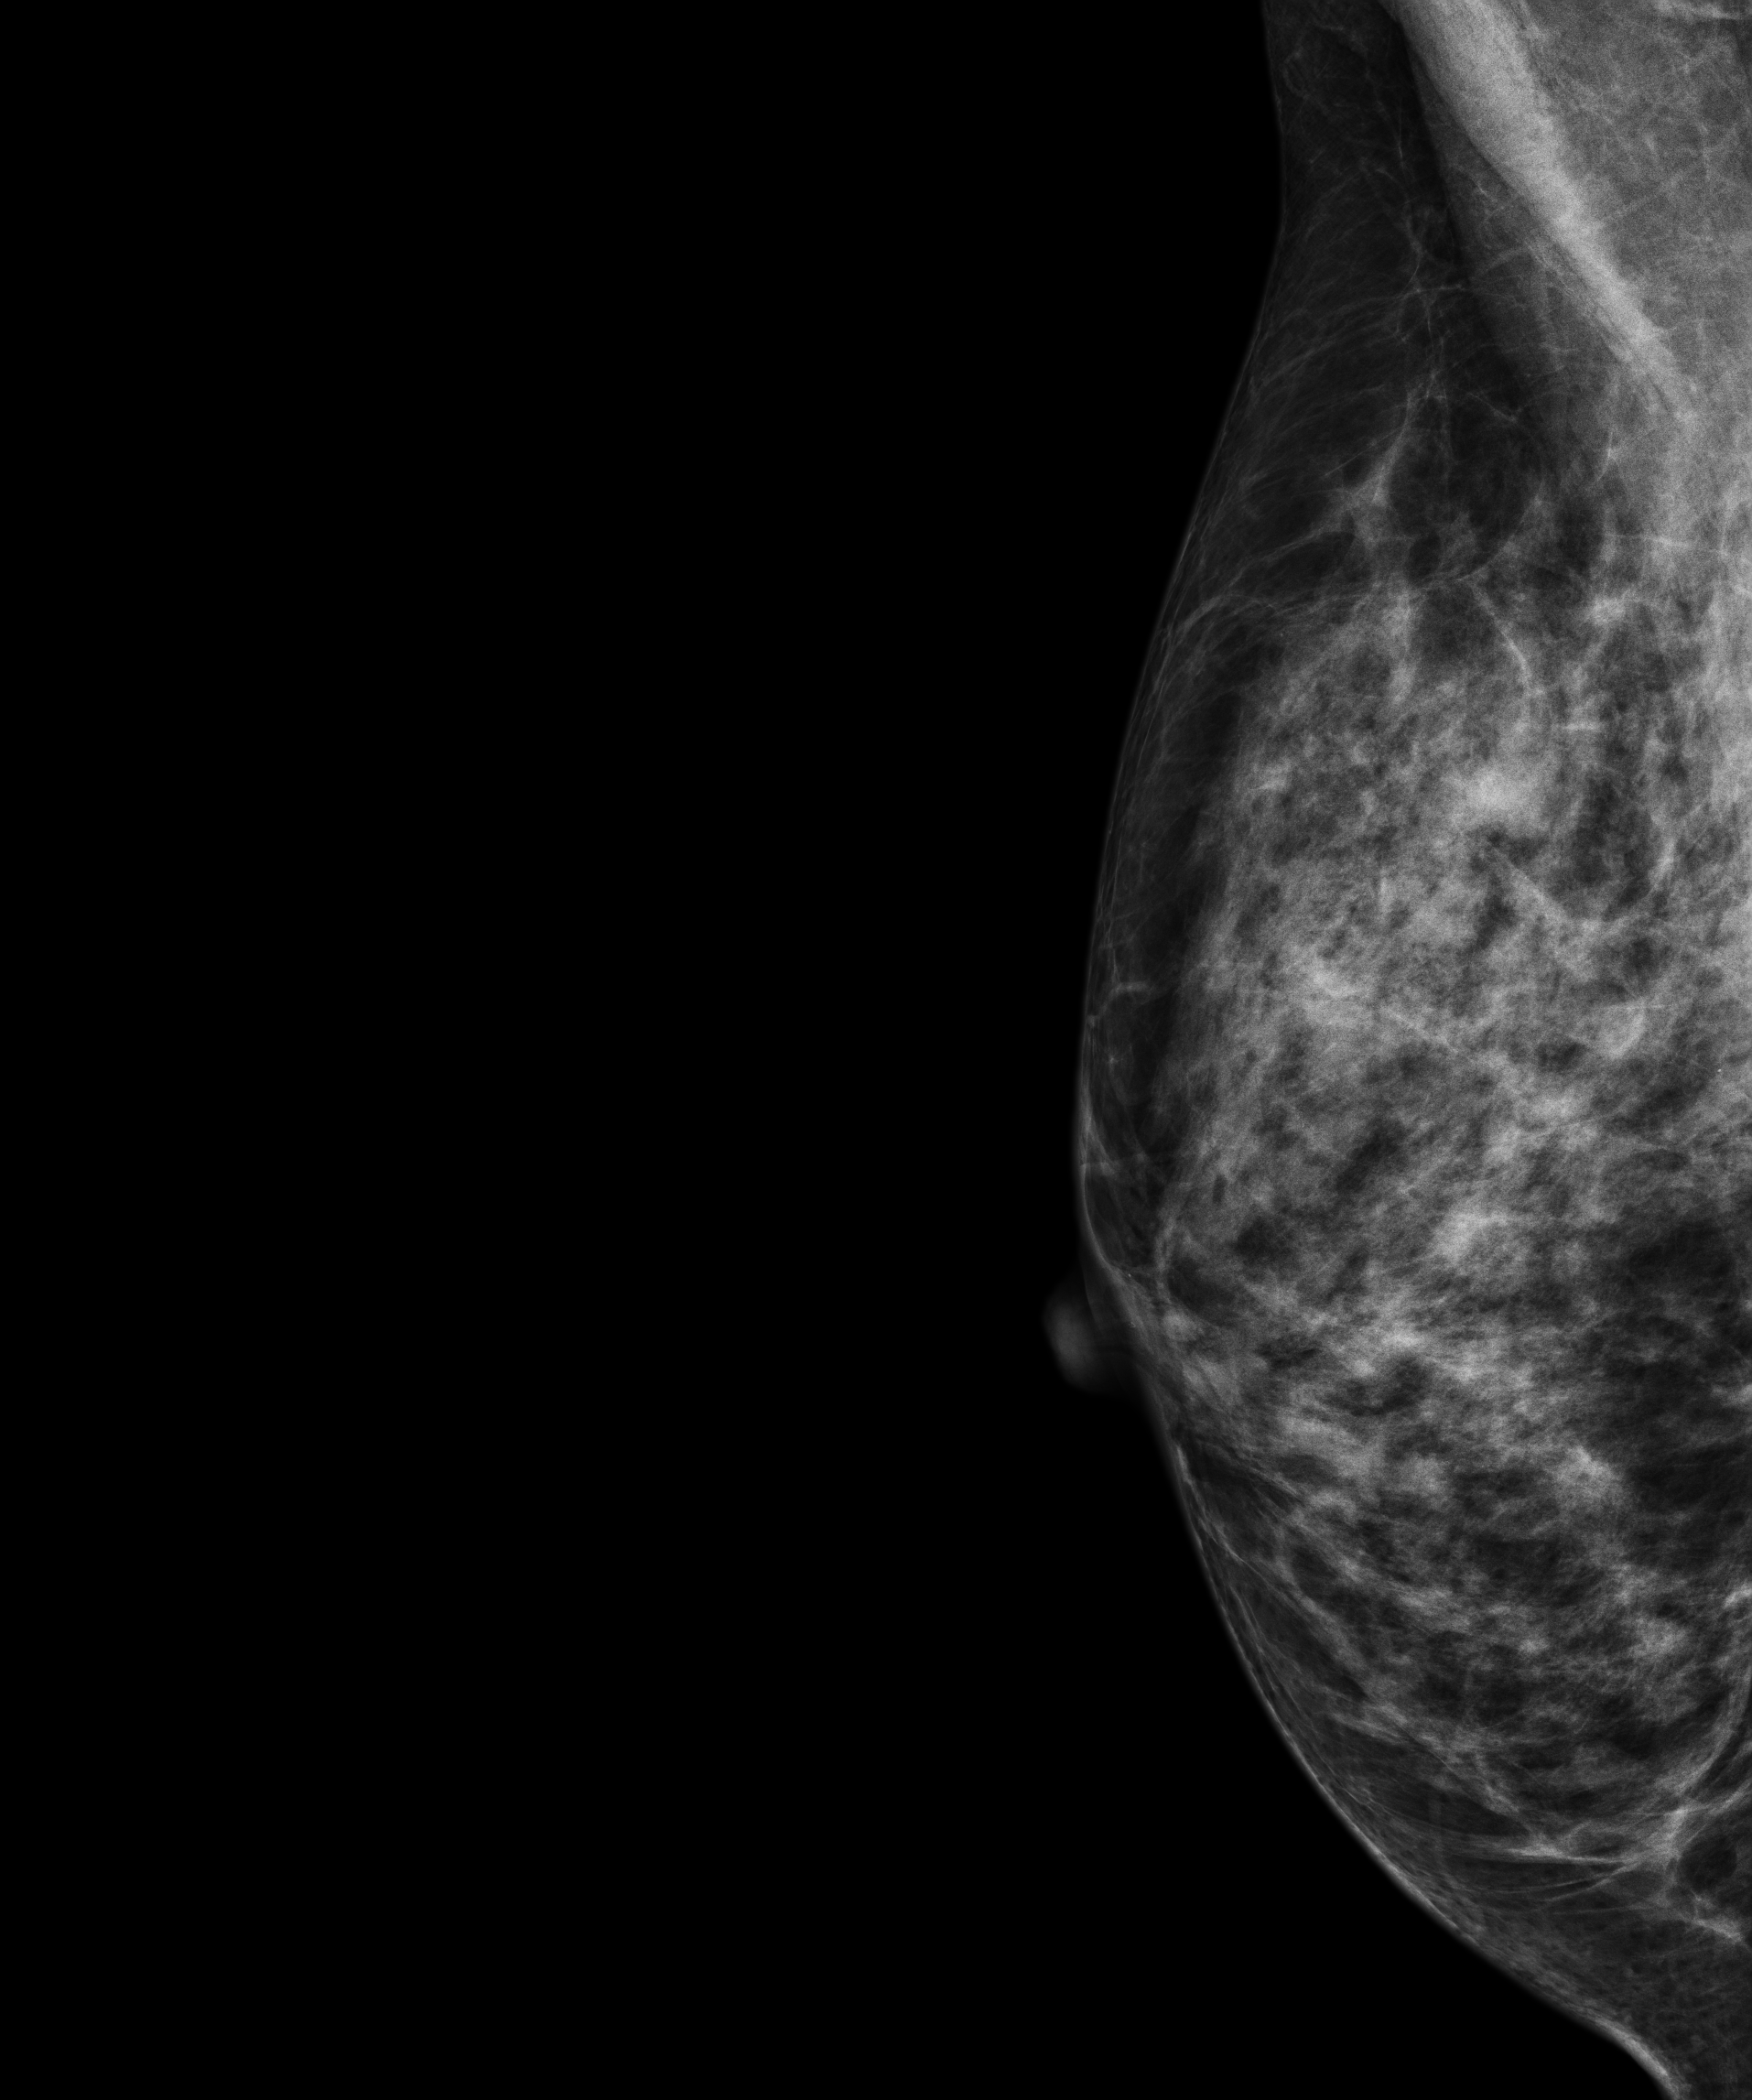
Digital mammogram (FFDM), right breast, mediolateral oblique (MLO) view, screening examination. Patient: female, 56 years.
- BI-RADS breast density category at the screening exam (both breasts, scale 1–4): 3
- final BI-RADS category for the screening round (tomosynthesis exam, both breasts): category 1
- recall: no recall after this screen